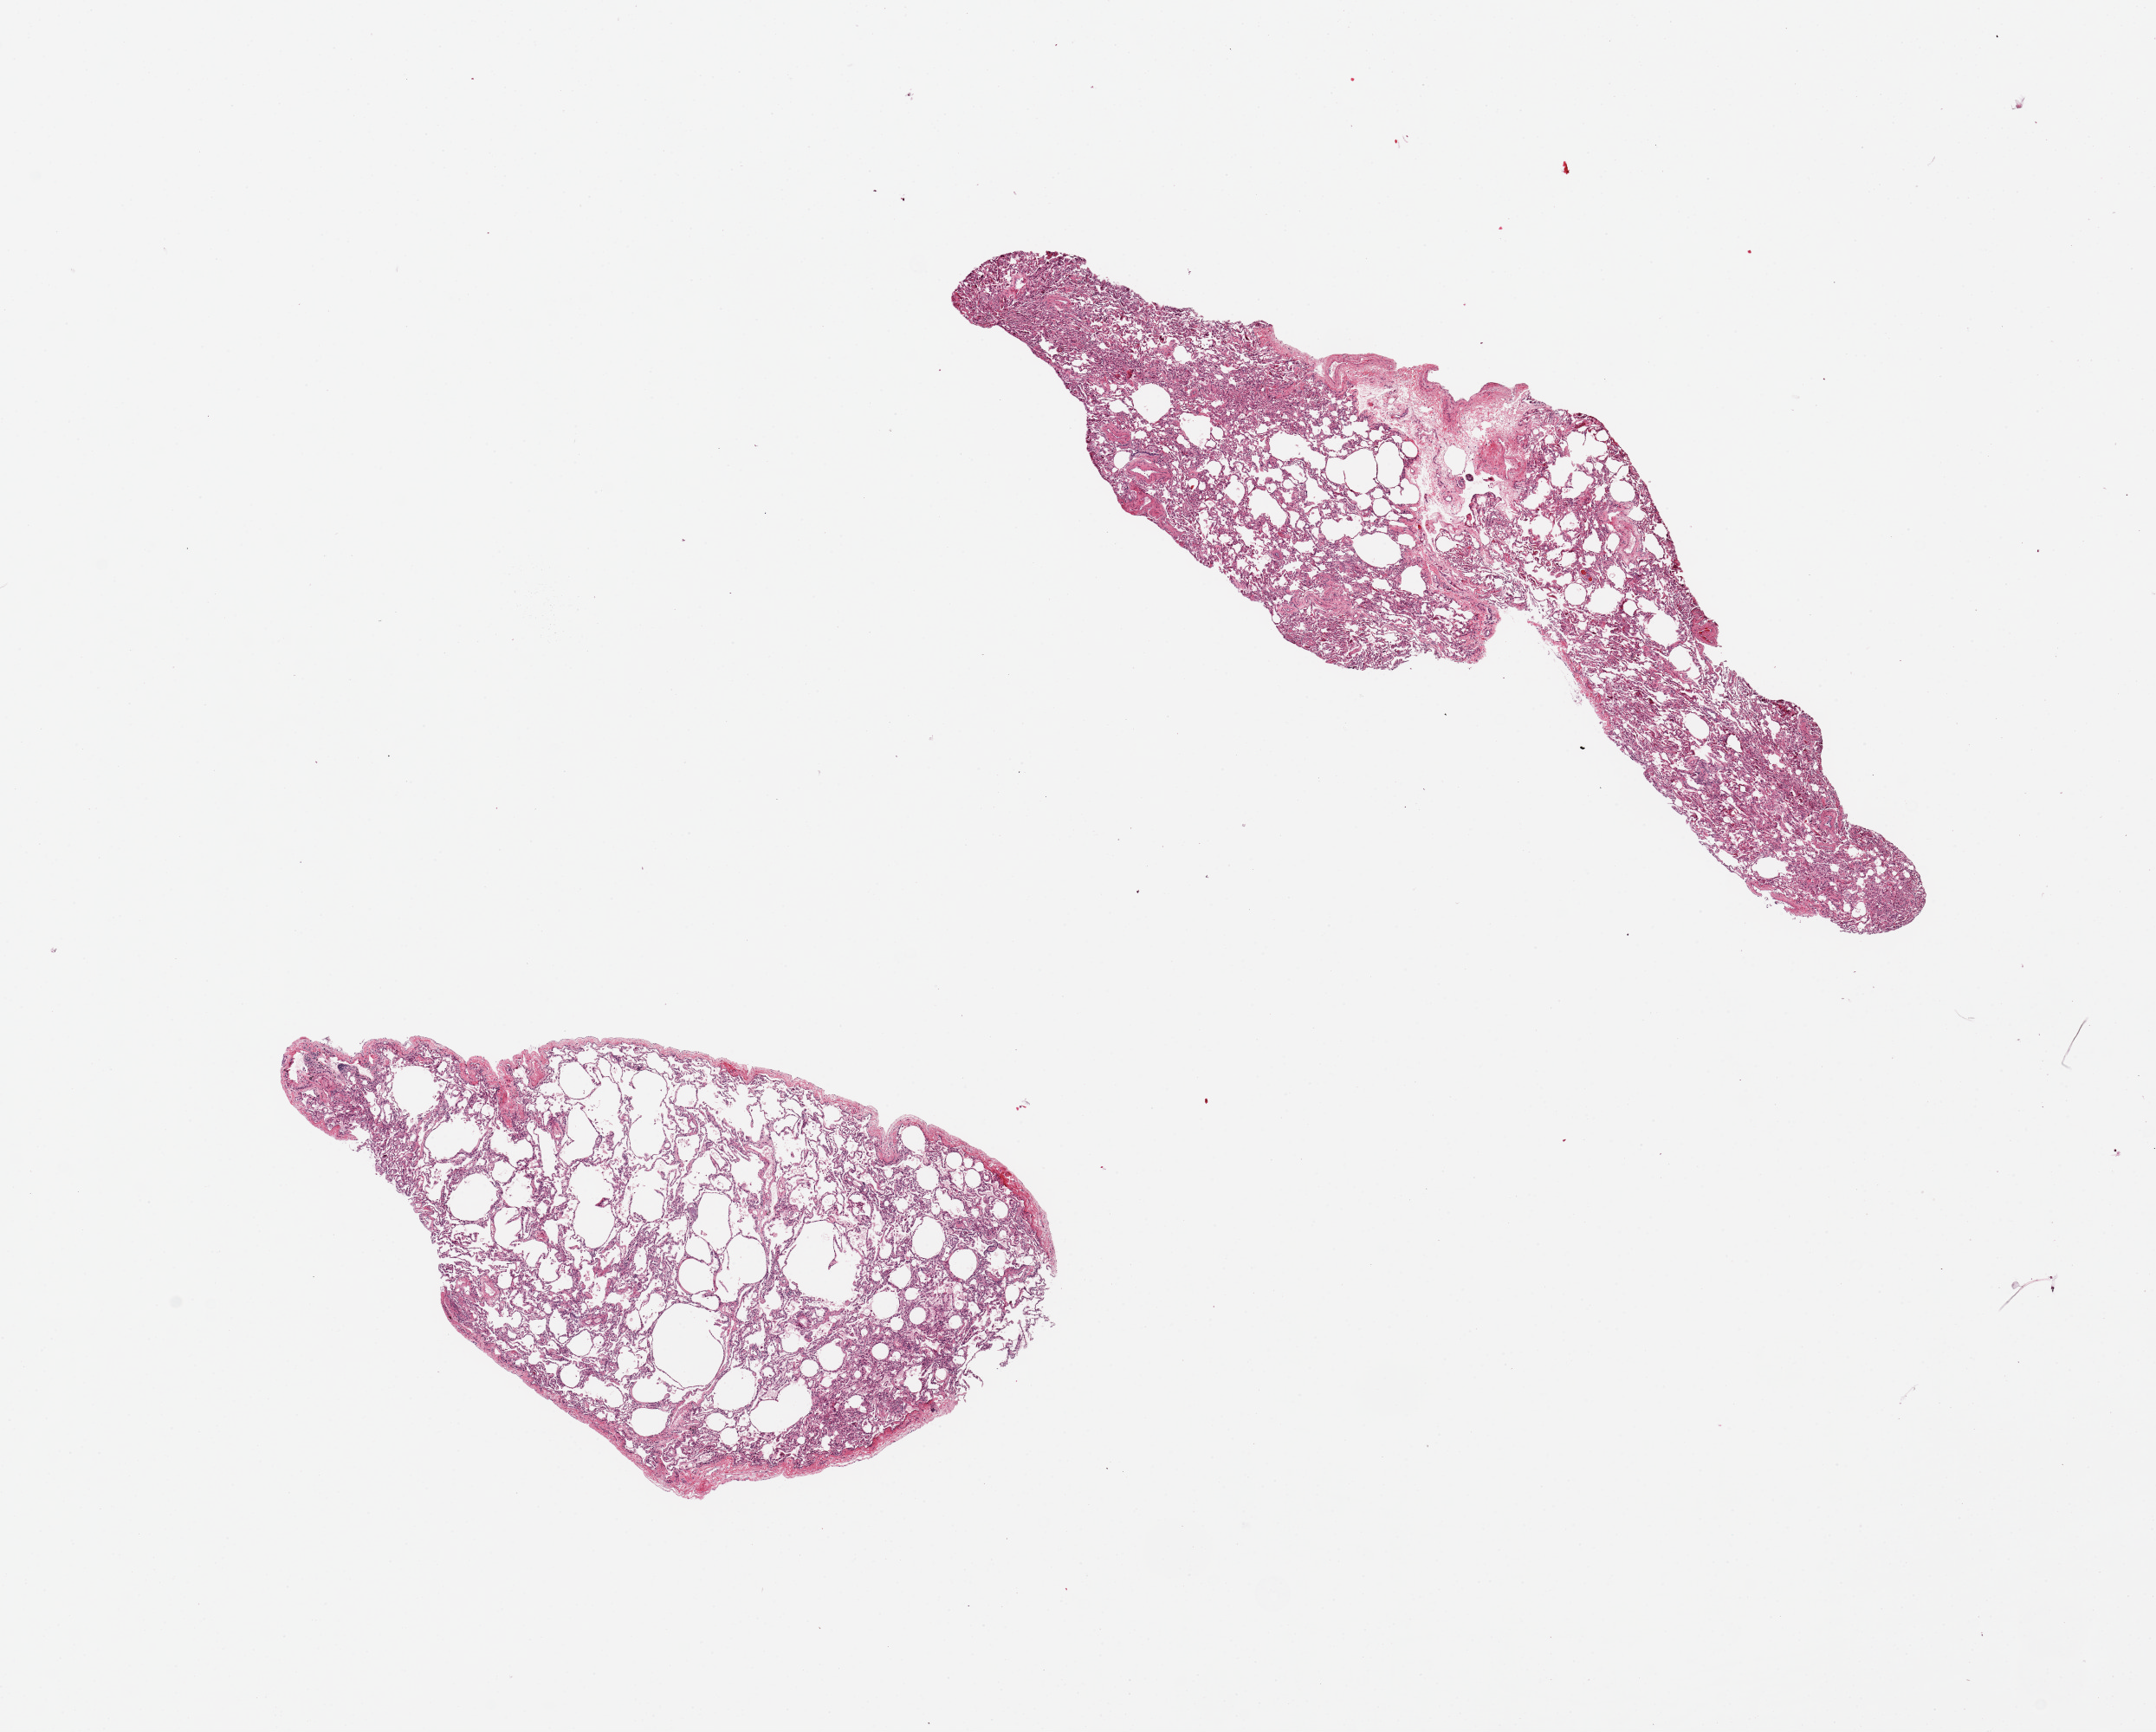
Digitized H&E-stained section, brightfield — a low-resolution overview of the entire scanned area, about 19.7 x 15.8 mm (acquisition: 20x scan), PAXgene-fixed paraffin-embedded (PFPE) section, sampled site (target tissue): lung, tissue donor sample. Donor: female.
Review note (as recorded): 2 pieces, emphysematous changes.